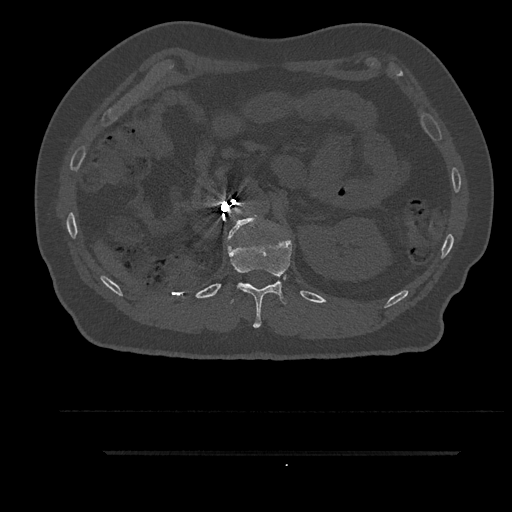
CT including the spine, one axial slice; slice 227 of 797 in the series (ordered by position); reconstruction kernel Br40s/3; 120 kVp; bone window (W 1800 / L 400 HU); 0.5 mm slice thickness; 512 × 512 image matrix, field of view 432 × 432 mm. Patient: male, 63 years. Case-level facts recorded for this patient, not image findings: primary cancer: renal.
Annotated regions visible in this slice (semi-automatically segmented with operator editing):
- L1 vertebra: bounding box (x1, y1, x2, y2) in pixels: (227, 215, 264, 241)
- T12 vertebra: (227, 229, 292, 328)